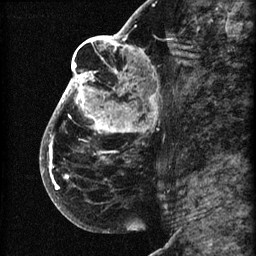
Breast MRI (dynamic contrast-enhanced), one sagittal slice; slice 37 of 60 in the series (ordered by position); 3 images stored at this slice position (order not interpretable as contrast timing); 1.5 T; TE 4.2 ms, TR 22.7 ms; 256 × 256 image matrix, field of view 180 × 180 mm. Female patient, age 48 years. Case-level facts recorded for this patient, not image findings: setting: breast cancer imaged before/during neoadjuvant chemotherapy; receptor status: triple-negative.
Structures marked on this image (semi-automatically segmented with operator editing):
- analysis volume of interest (the breast-tissue region the enhancement analysis was run in; not a lesion): box from (x=44, y=30) to (x=173, y=207) px
- tumour enhancement mask (voxels above the 90 % enhancement threshold inside the analysis volume of interest): (x=44, y=30)–(x=156, y=190)